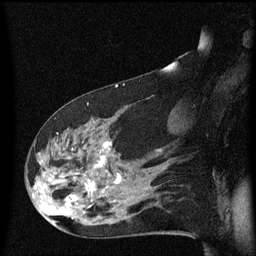
Breast MRI (dynamic contrast-enhanced), one sagittal slice; dynamic contrast-enhanced series, image 2 of 3 at this slice position (ordered by acquisition); 1.5 T; TE 4.2 ms, TR 8.4 ms; 2 mm slice thickness; 256 × 256 image matrix, field of view 200 × 200 mm. Female patient, age 48 years.
Structures marked on this image (semi-automatic segmentation, software-assisted and operator-edited):
- analysis volume of interest (the breast-tissue region the enhancement analysis was run in; not a lesion): bounding box <31,116,134,225> (left, top, right, bottom; pixels)
- tumour enhancement mask (voxels above the 70 % enhancement threshold inside the analysis volume of interest): <65,142,121,205>